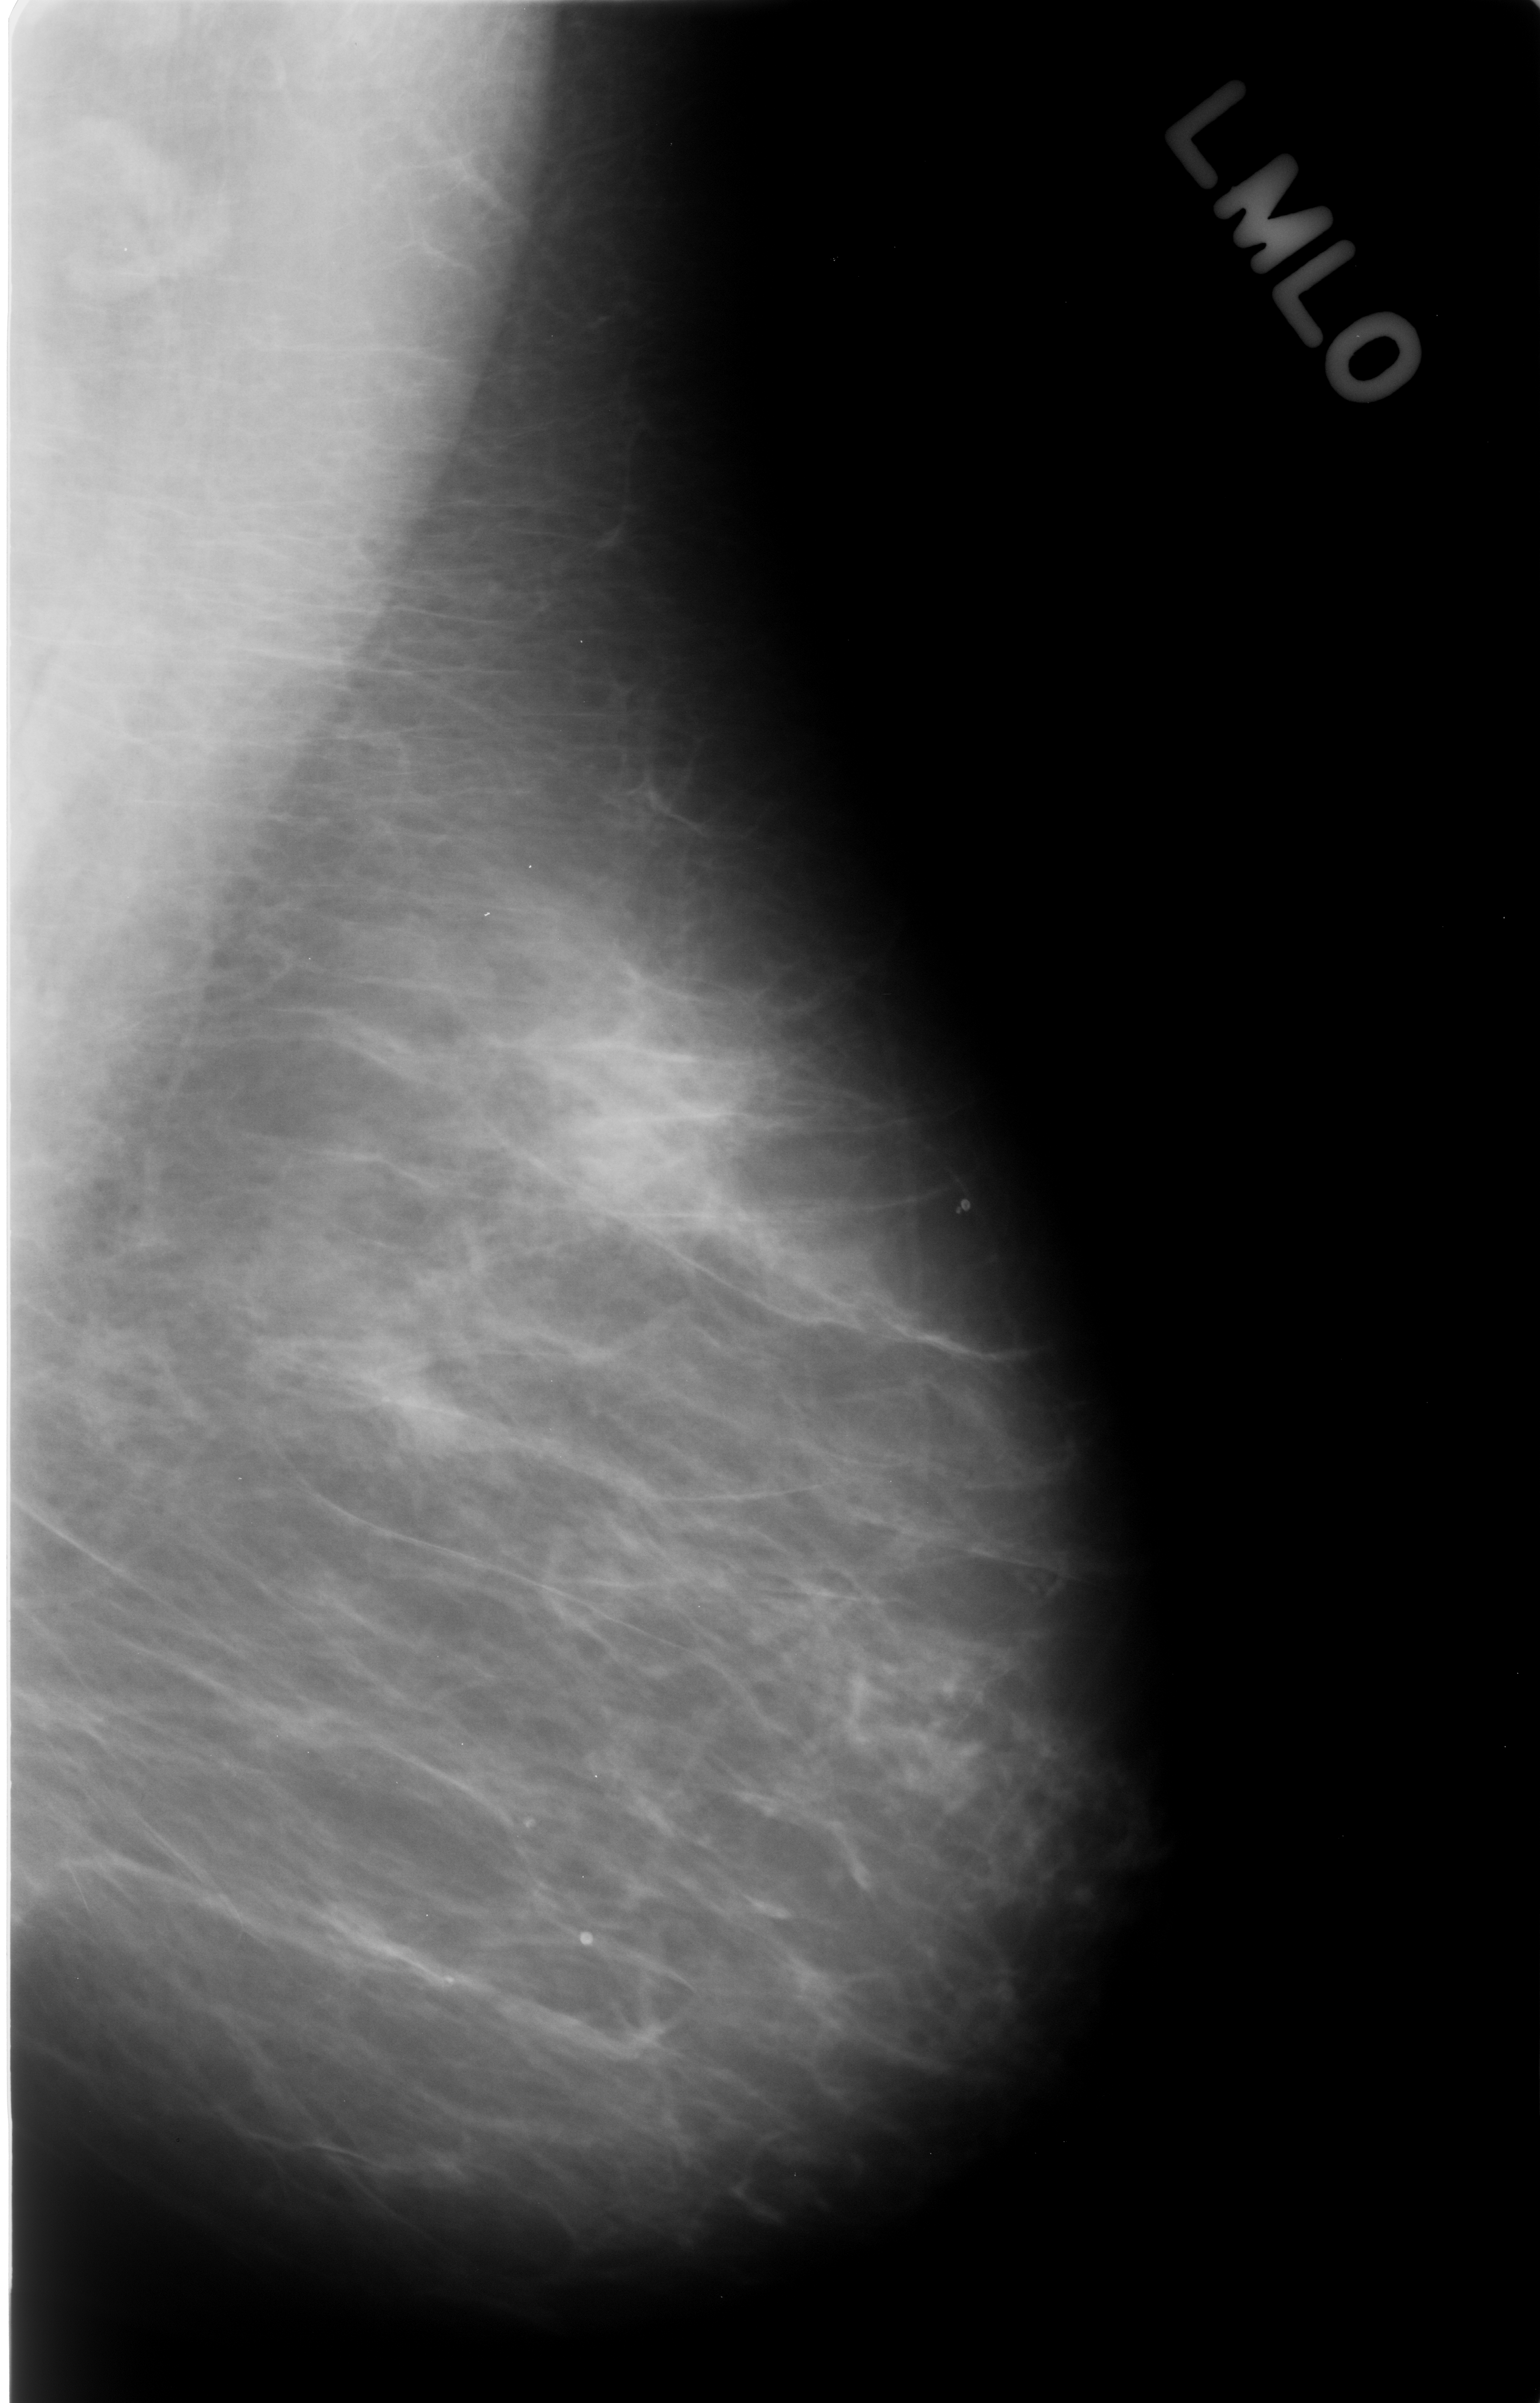
Digitized screen-film mammogram; left breast; MLO view; BI-RADS breast density category 1 (scale 1–4).
Finding: mass, shape oval, margins circumscribed; BI-RADS assessment category 3; subtlety rating 3 on a 1 (subtle) to 5 (obvious) scale; benign; no additional work-up was recommended (benign without callback).